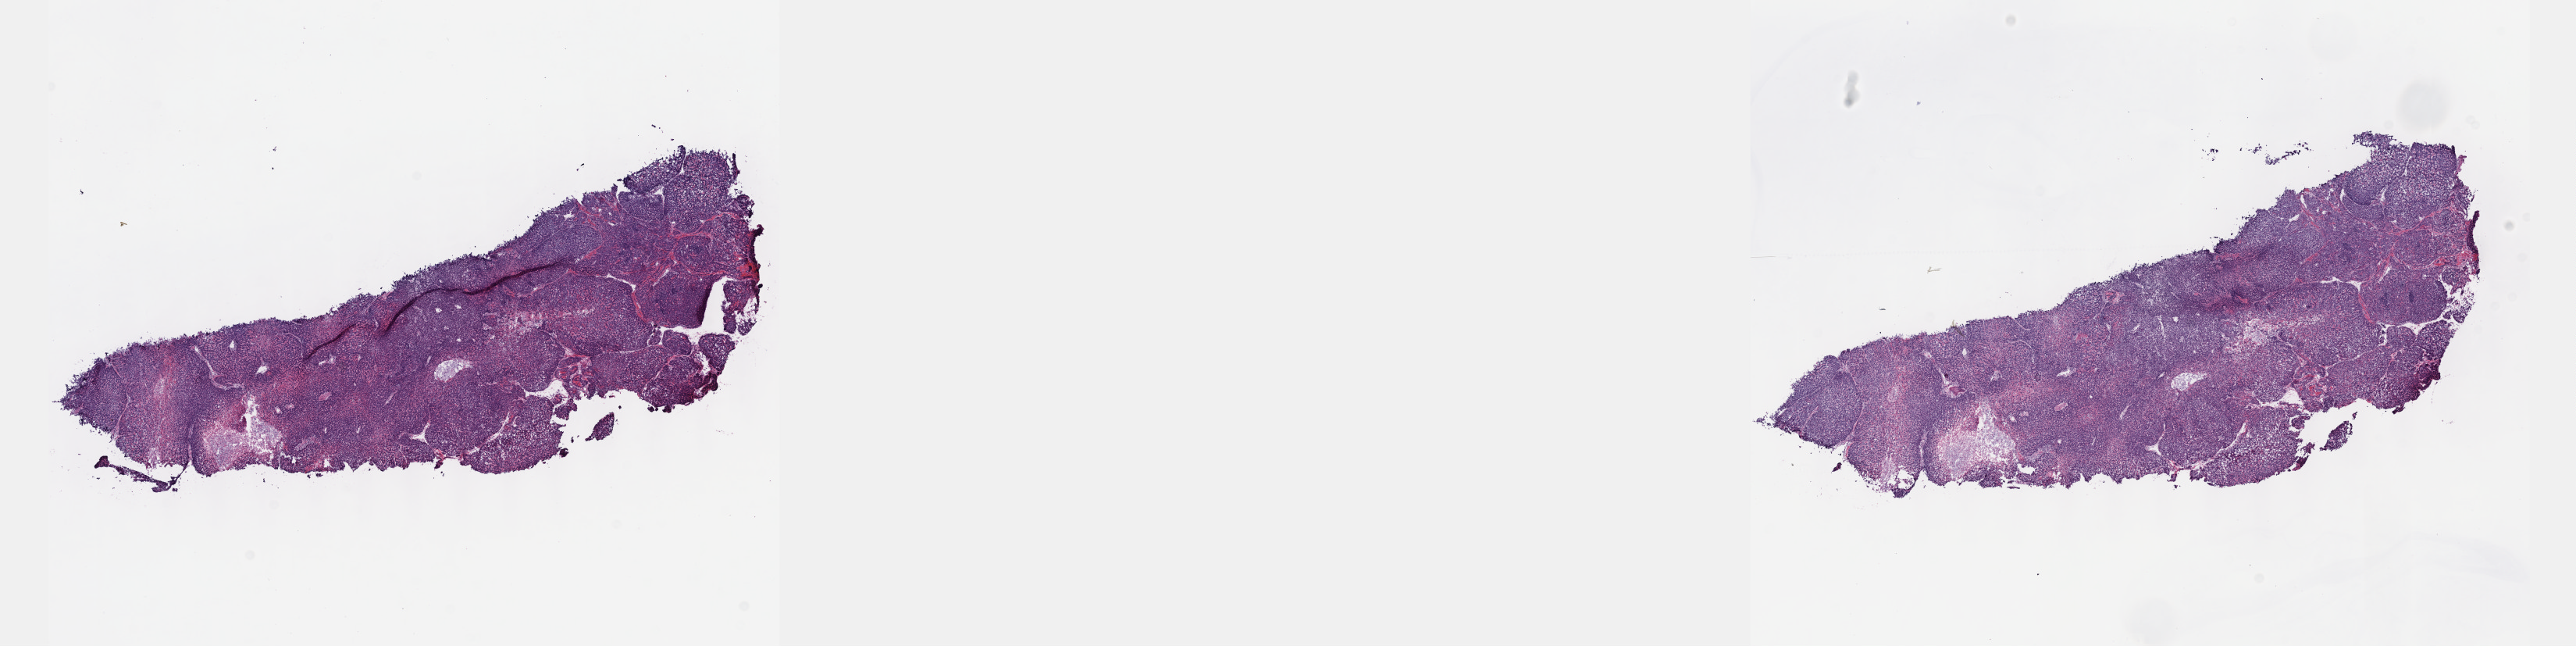
Digitized H&E-stained tissue section (whole slide) — shown as a low-resolution overview of the whole scanned area (about 26.7 x 6.7 mm). Frozen section. Primary tumour sample from the thymus. Male patient; age at initial diagnosis 64 years.
Pathologic diagnosis: Thymoma, type A, malignant (anterior mediastinum).